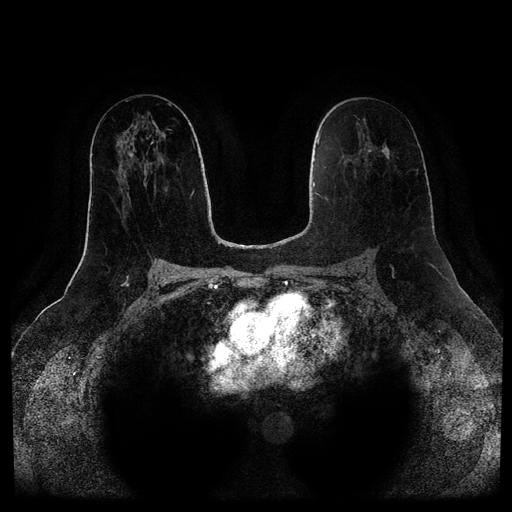
Breast MRI (dynamic contrast-enhanced, multi-phase), one axial slice. Position 48 of 116 along the scan axis. Dynamic contrast-enhanced series, time point 2 of 5 at this slice position (early post-contrast). 1.5 T. TE 2.6 ms, TR 5.2 ms. 2 mm slice thickness. 512 × 512 image matrix, field of view 380 × 380 mm. Patient: female, 57 years.
Outlined on this slice (semi-automatically segmented with operator editing):
- breast lesion (labelled benign in the annotation): bounding box (x1, y1, x2, y2) in pixels: (382, 145, 389, 158)